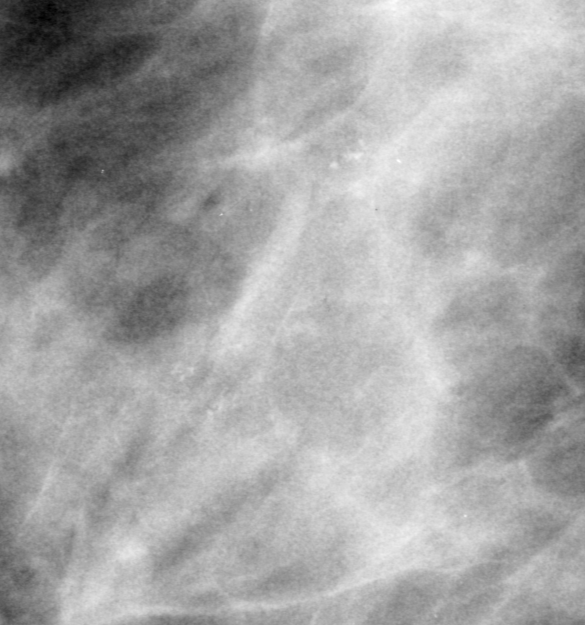
Crop from a digitized film mammogram around one marked abnormality, right breast, MLO view.
Calcifications, morphology amorphous, distribution clustered; BI-RADS assessment category 0 (incomplete: needs additional imaging); subtlety rating 2 on a 1 (subtle) to 5 (obvious) scale; pathology result (as recorded, not read from the image): benign.